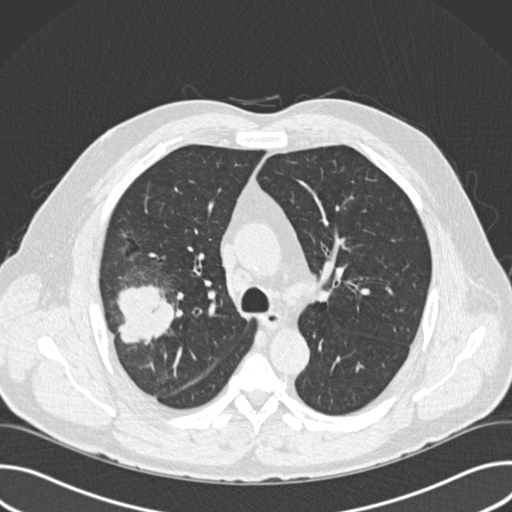
Low-dose screening chest CT, one axial slice; slice 109 of 157 in the series (ordered by position); reconstruction kernel B30f; 120 kVp; lung window (W 1500 / L -600 HU); 2 mm slice thickness; 512 × 512 image matrix, field of view 380 × 380 mm.
Annotated regions visible in this slice (manually delineated by an expert):
- lesion 1 (tumor, upper lobe of right lung): bounding box <117,285,175,344> (left, top, right, bottom; pixels)